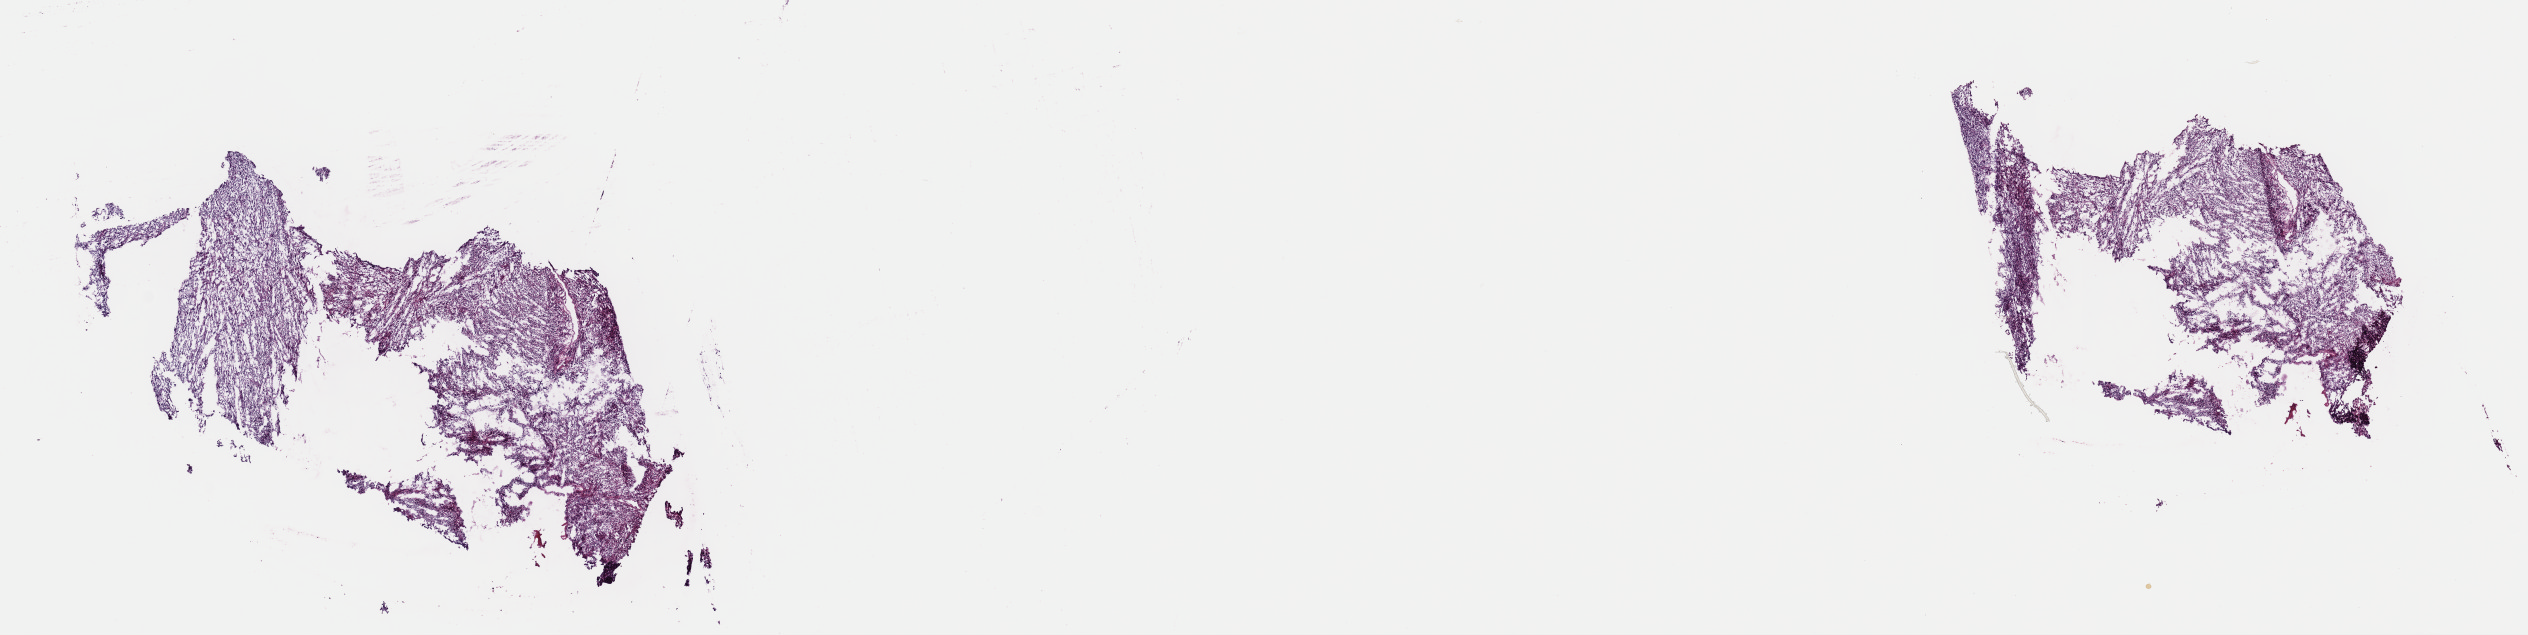
Whole-slide histology image, Hematoxylin and eosin (H&E) stained — low-resolution overview of the scanned area, about 20.0 x 5.0 mm, frozen section from the top of the tissue portion, retroperitoneum and peritoneum, primary tumour sample. Patient: female, age at initial diagnosis 53 years. Slide review estimates, as recorded: tumour cells 100%, tumour nuclei 80%.
Histologic diagnosis: Leiomyosarcoma, NOS (retroperitoneum).